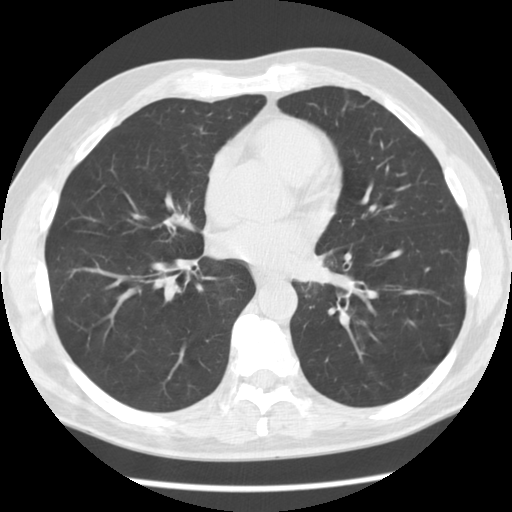
Axial slice from a low-dose chest CT screening exam, first (baseline) screen, lung window (W 1500 / L -600 HU), slice 64 of 112 in the series, 512 × 512 image matrix. Male participant, aged 55 years at enrolment.
Expert reader's lesion annotation, box from (x=282, y=235) to (x=347, y=301) px. Screening reader's record for this exam: no non-calcified nodule ≥4 mm recorded. Official screen result: negative screen, minor abnormalities not suspicious for lung cancer. Lung cancer was diagnosed 223 days after this screen: squamous cell carcinoma, NOS, left lower lobe, moderately differentiated (G2), stage IV (AJCC 6th edition), 51 mm at pathology.